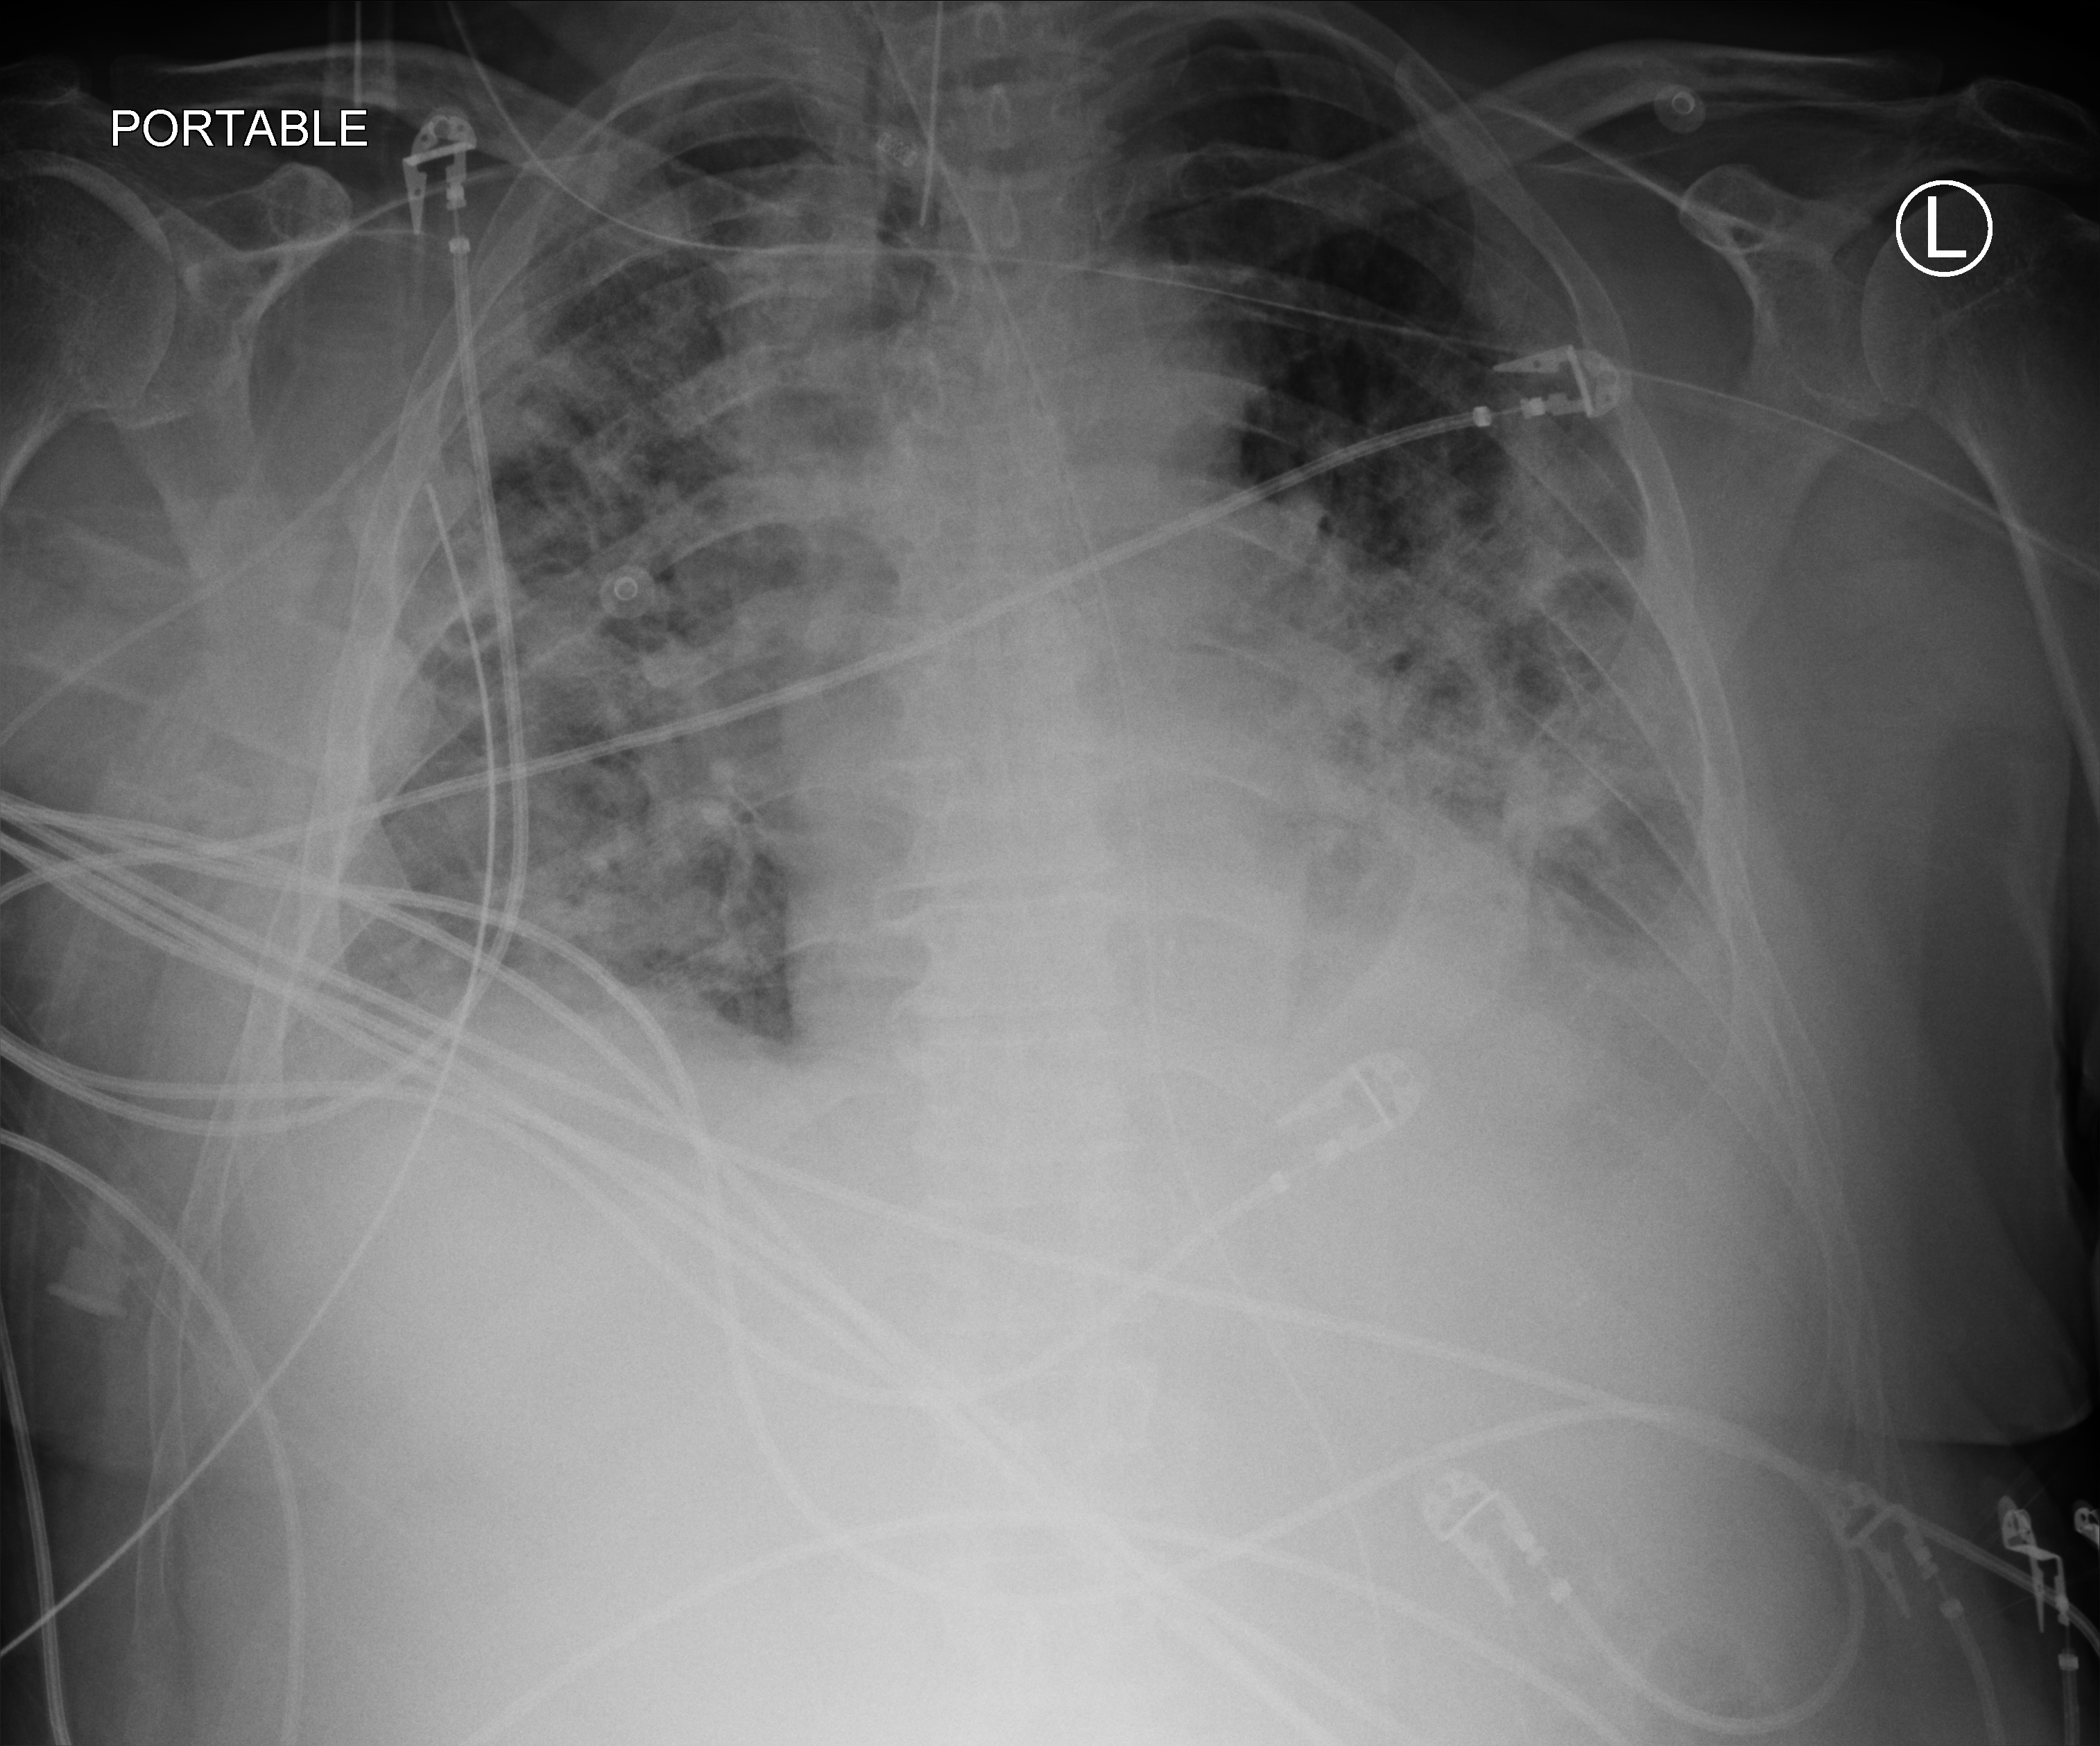
Bedside chest radiograph (computed radiography); anteroposterior (AP) projection. Patient hospitalised with COVID-19; male, aged 60–74 years.
From the hospital-stay record, not from the radiograph (when in the stay this image was taken is not recorded): admitted to intensive care during this hospital stay: yes; mechanically ventilated during this hospital stay: yes.